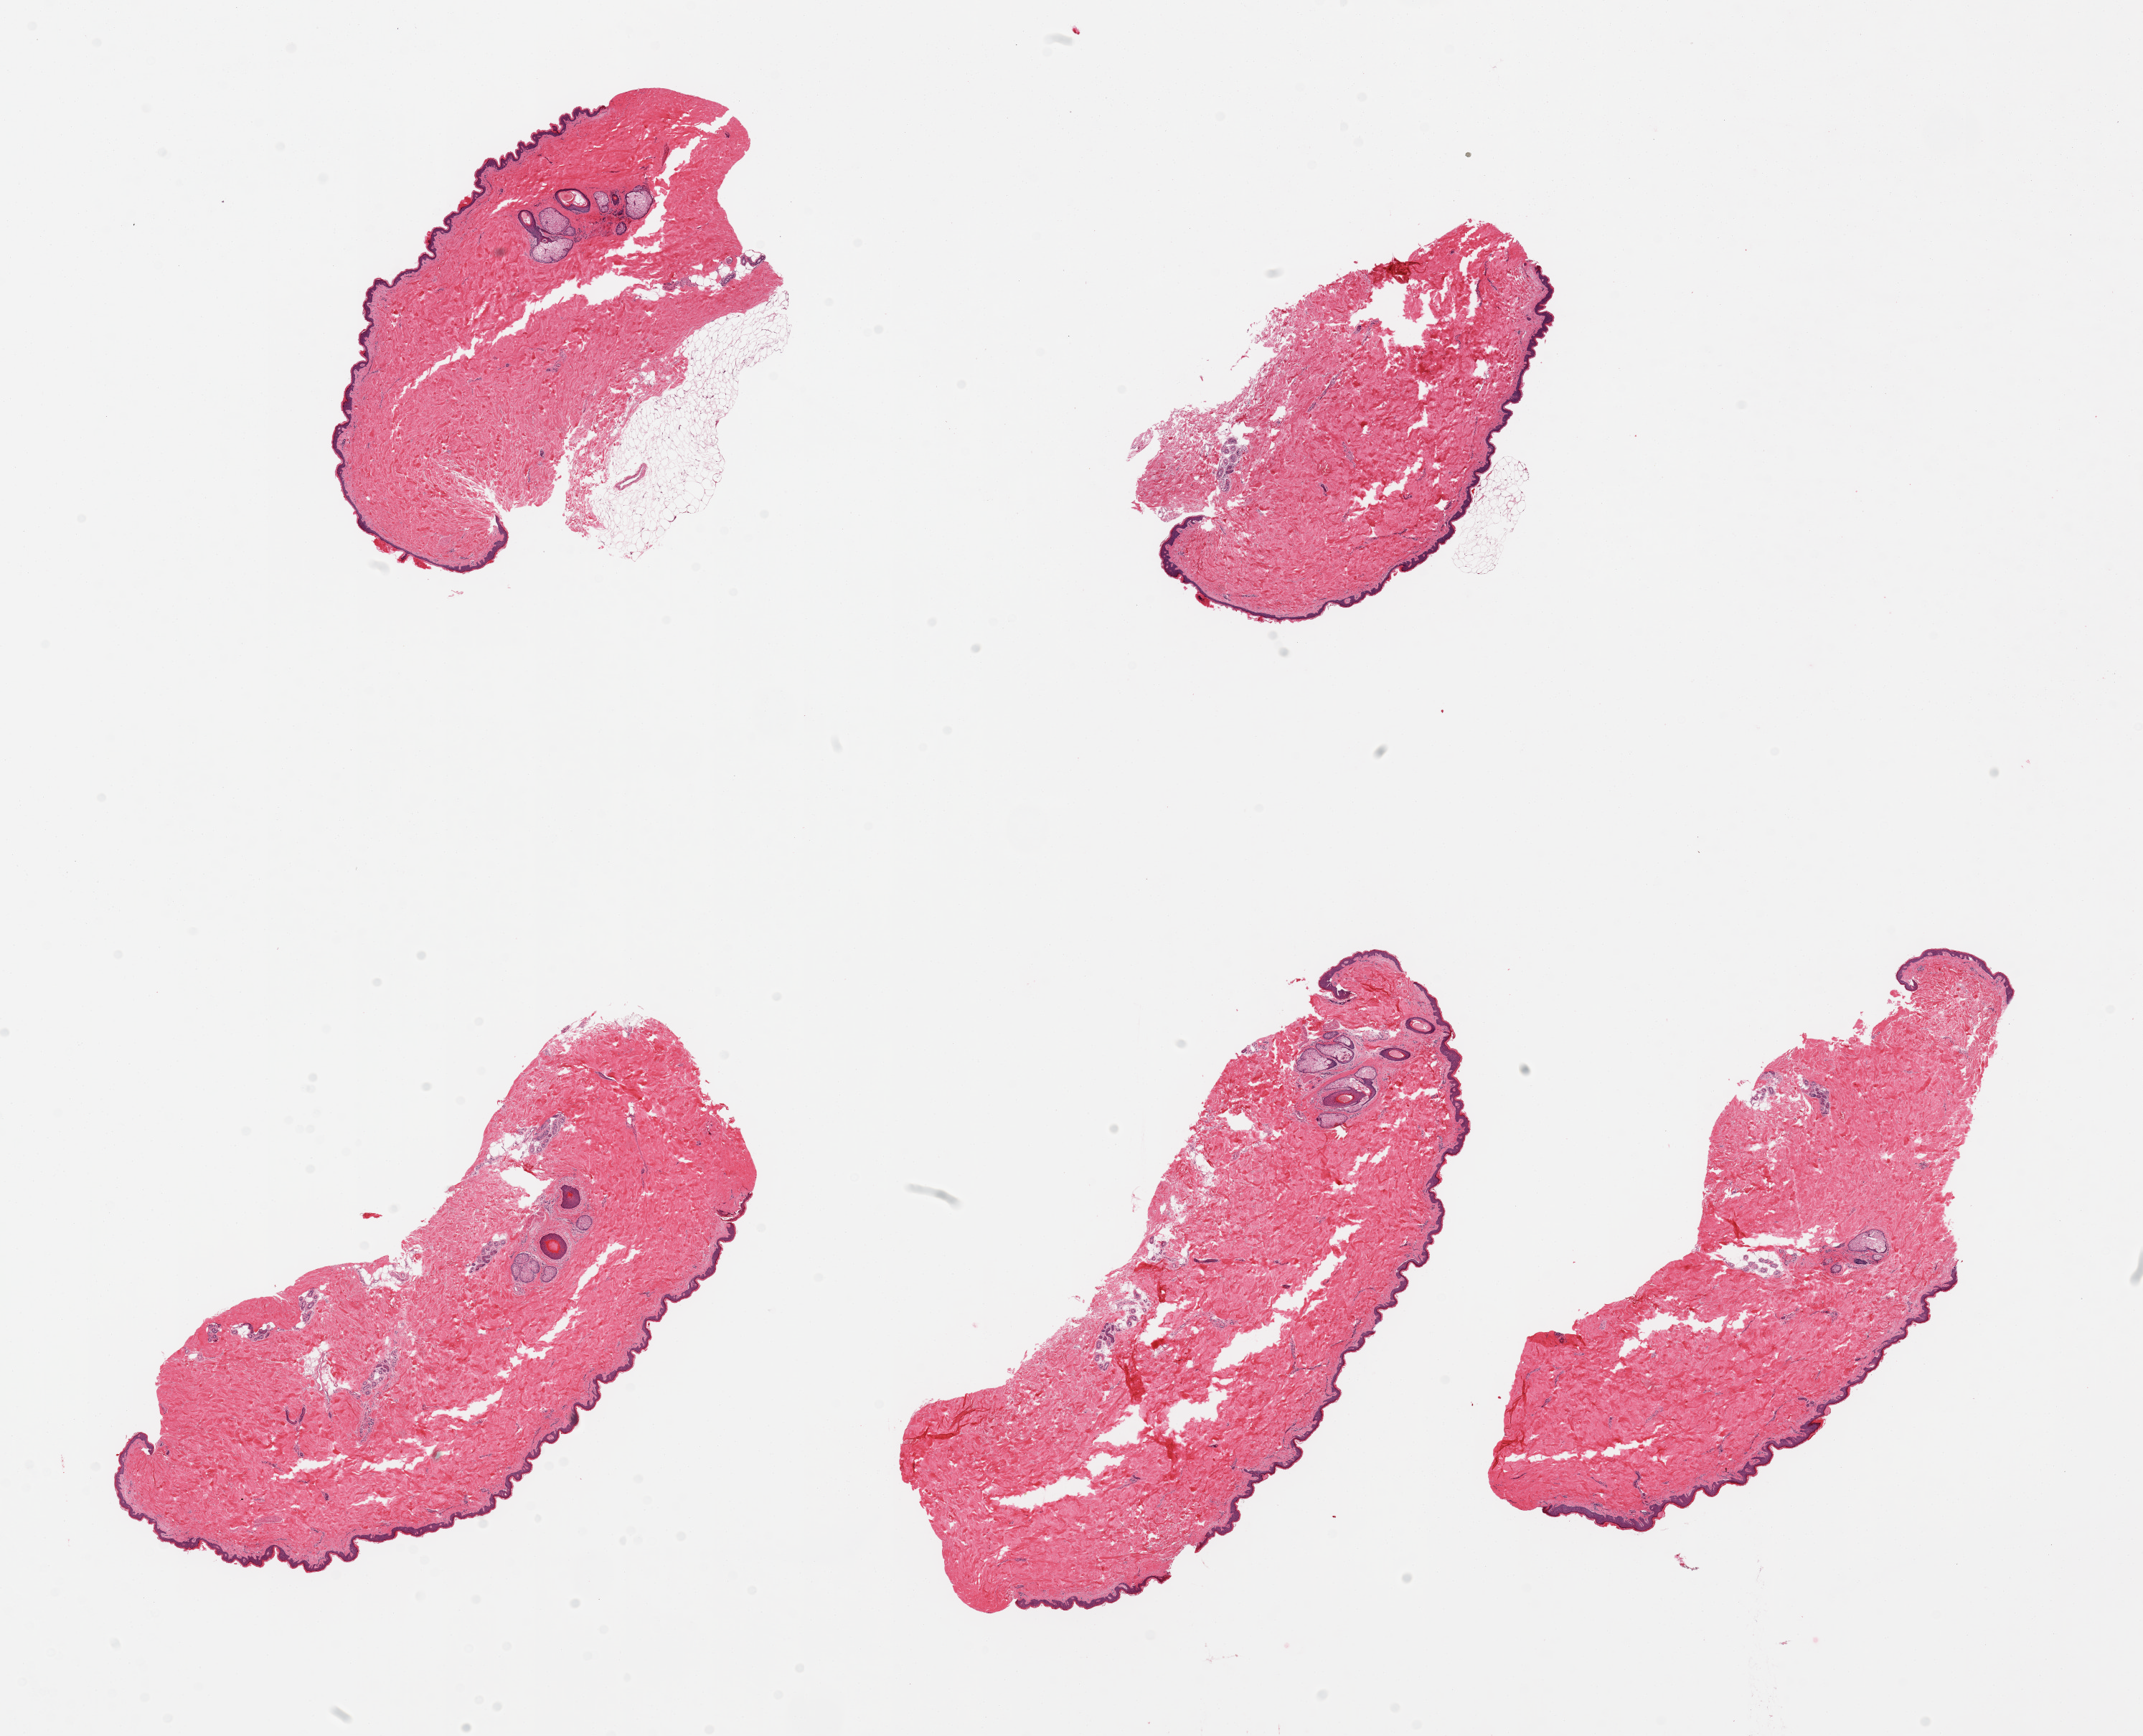
Digitized H&E-stained section — whole scanned area (about 23.6 x 19.1 mm) shown as a low-resolution overview, PAXgene-fixed, paraffin-embedded tissue, section of skin of suprapubic region (target tissue), tissue donor sample. Donor sex: male.
• pathologist's review note for this sample: 6 pieces, no significant dermal fat; squamous epithelium is ~45-50 microns